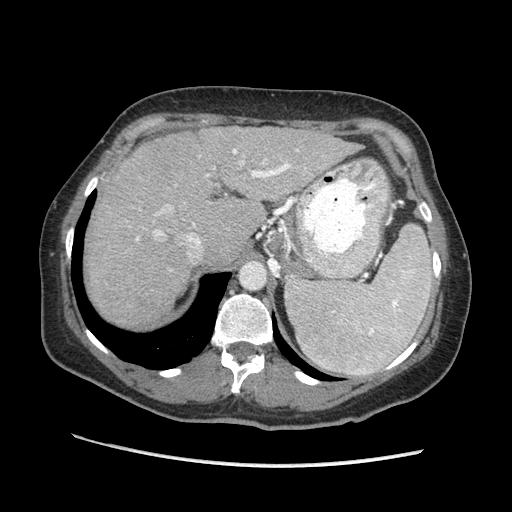
Contrast-enhanced abdominal CT (liver protocol), one axial slice; position 142 of 170 along the scan axis; reconstruction kernel STANDARD; 140 kVp; soft-tissue window (W 400 / L 40 HU); 2.5 mm slice thickness; 512 × 512 image matrix, field of view 360 × 360 mm. From the clinical record (not read from this slice): diagnosis: hepatocellular carcinoma (patient treated with transarterial chemoembolisation; whether this scan precedes or follows treatment is not stated here); TNM stage (as recorded): Stage-II; Child-Pugh class: A; tumour differentiation: no biopsy; tumour nodularity: multinodular.
Annotated regions visible in this slice (semi-automatically segmented with operator editing):
- abdominal aorta: box from (x=241, y=264) to (x=265, y=289) px
- liver parenchyma outside the tumour (the mass and vessels are separate outlines, so this box may not span the whole liver): (x=86, y=126)–(x=358, y=326)
- liver vessels: (x=136, y=149)–(x=306, y=257)